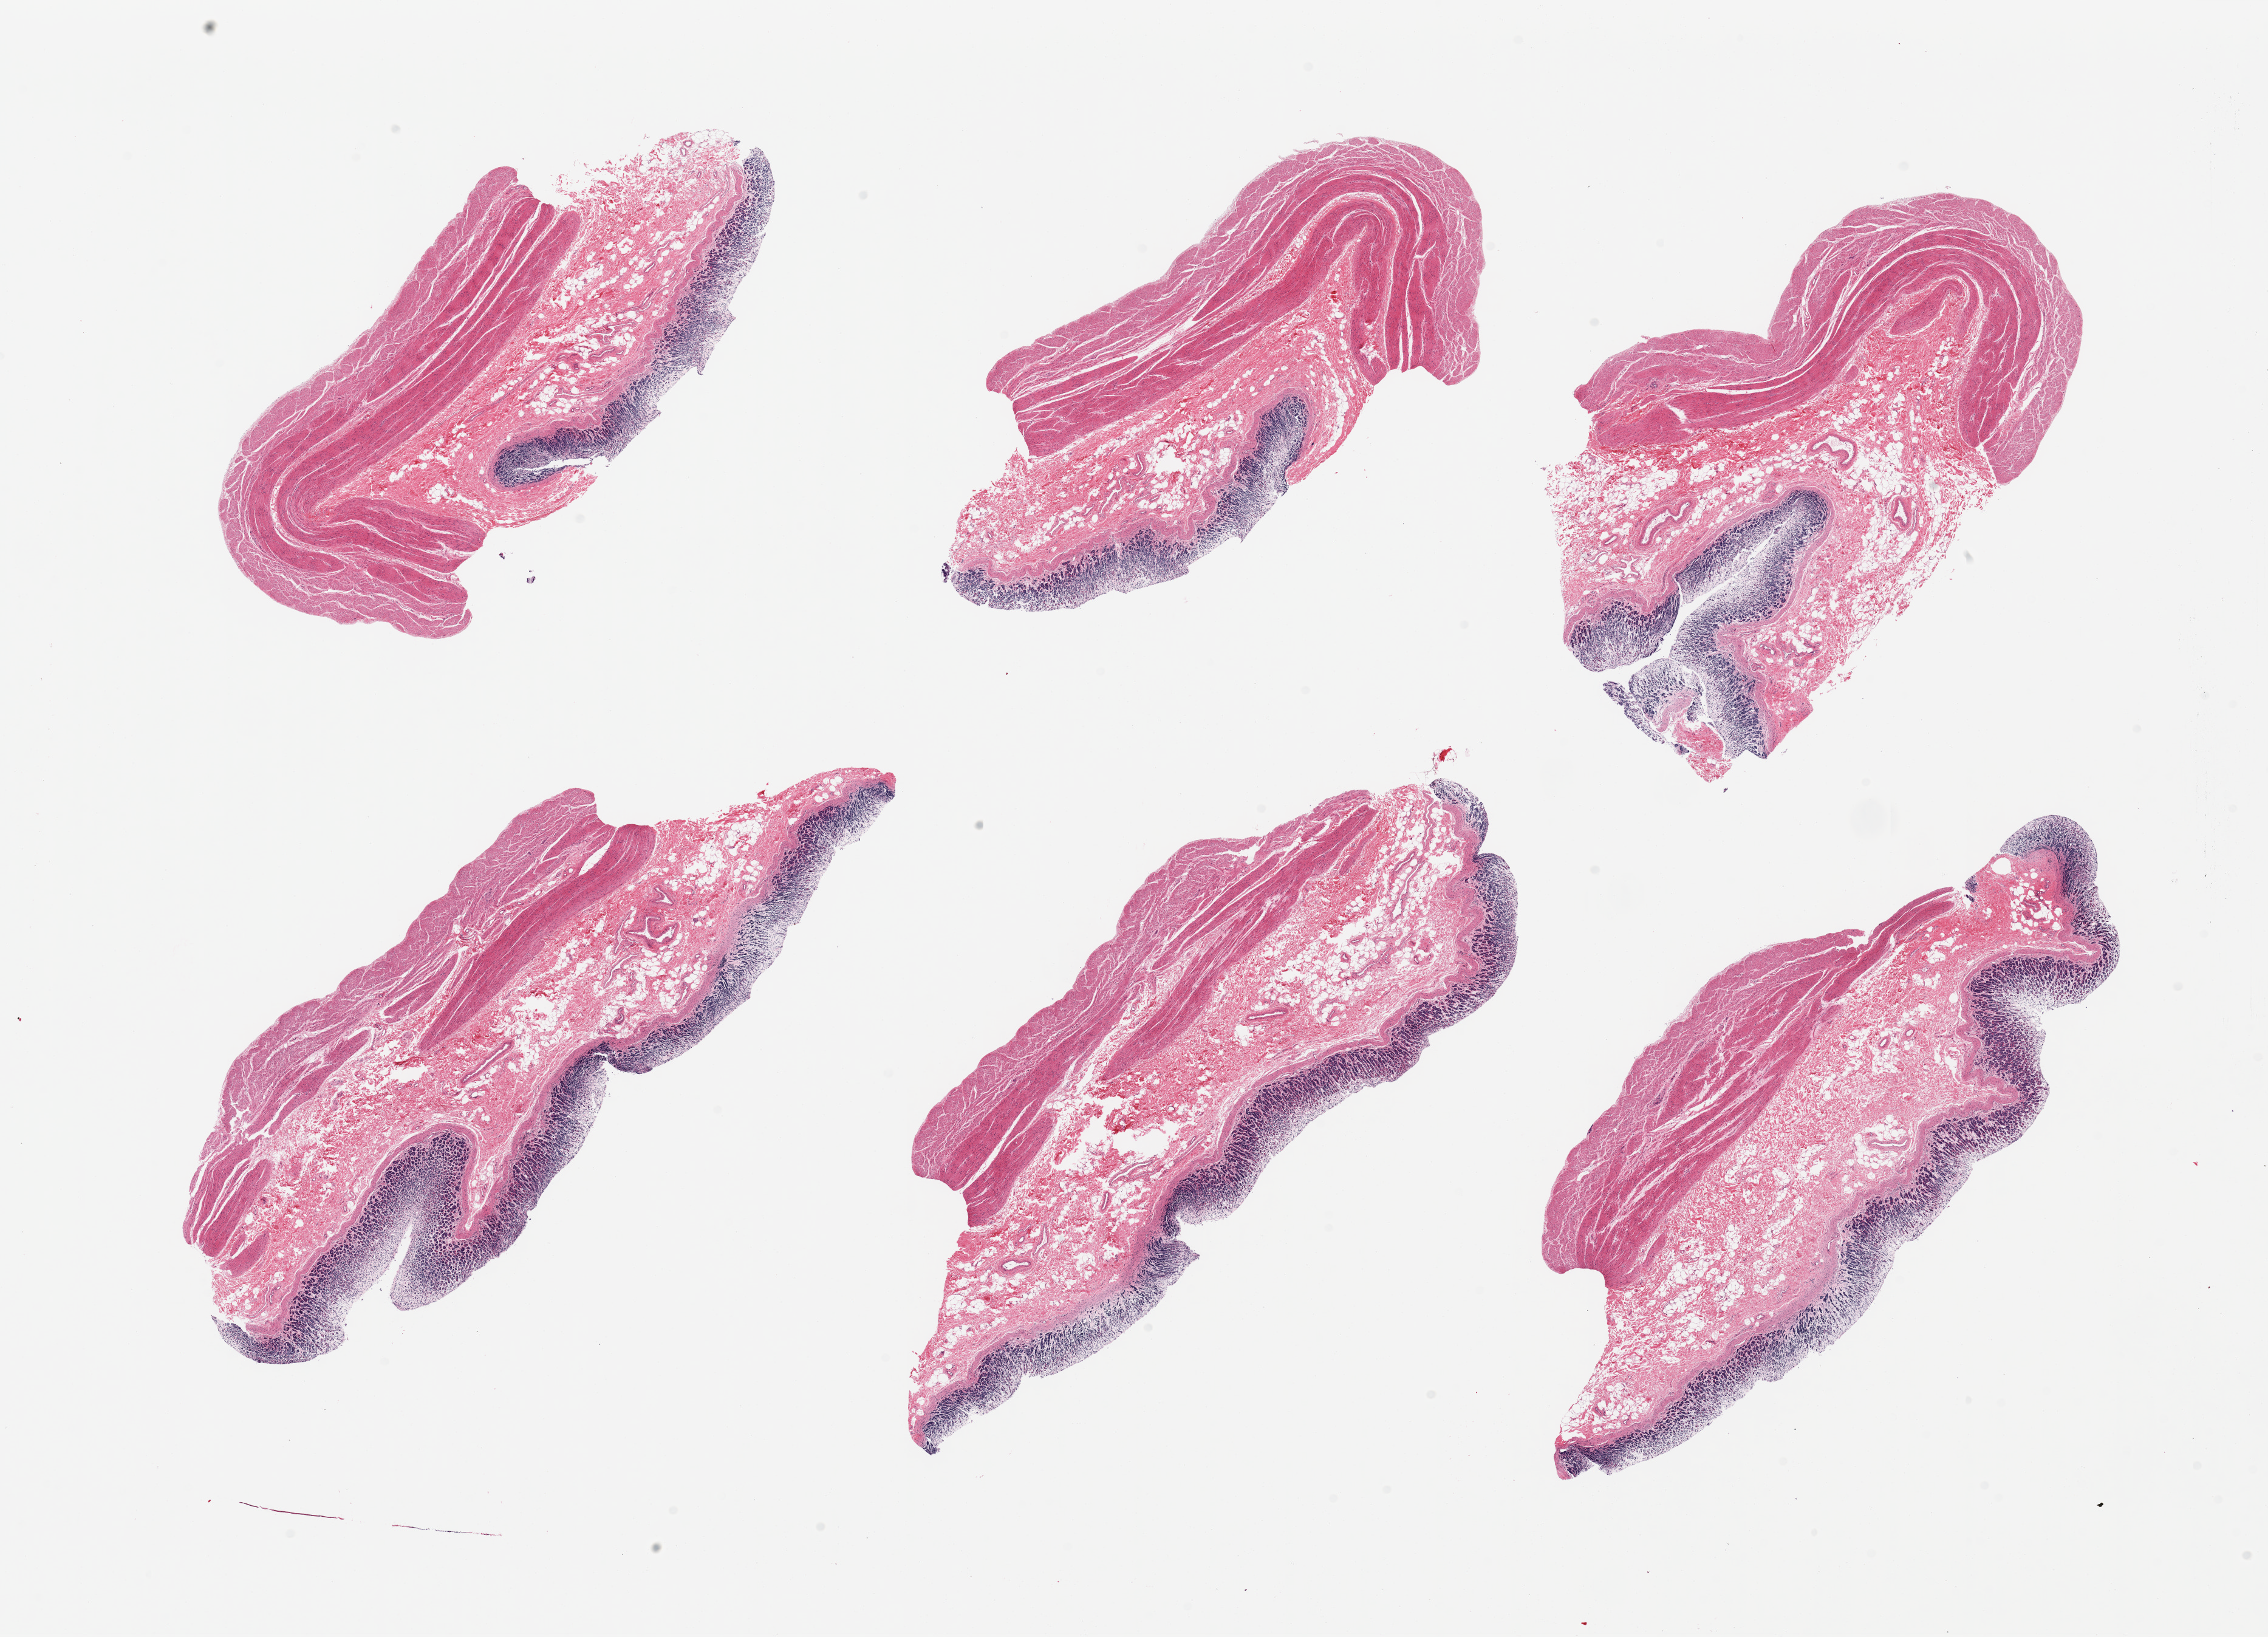
Whole-slide image, hematoxylin and eosin (H&E) stain, whole scanned area (about 29.5 x 21.3 mm) shown as a low-resolution overview, PAXgene-fixed, paraffin-embedded tissue, target tissue: stomach, tissue donor sample. Male donor.
Pathologist's review note for this sample: 6 pieces; mucosa variably preserved.